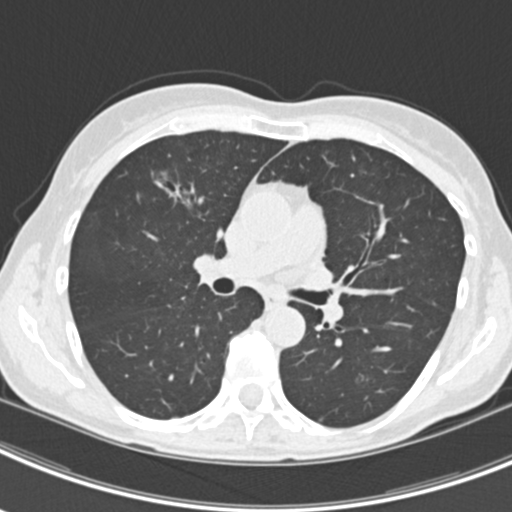
Chest CT (low-dose screening protocol), one axial image, second screening round (one year after baseline), lung window (W 1500 / L -600 HU), 2 mm slice thickness, 120 kVp, slice 82 of 219 in the series, 512 × 512 image matrix, field of view 298 × 298 mm. Female participant, aged 63 years at enrolment. Current smoker at enrolment.
• Expert-annotated lung lesion, bounding box <155,165,214,220> (left, top, right, bottom; pixels).
• The screening reader recorded 9 non-calcified nodules or masses ≥4 mm on this exam; which of them this box marks is not recorded.
• Official screen result: positive, other.